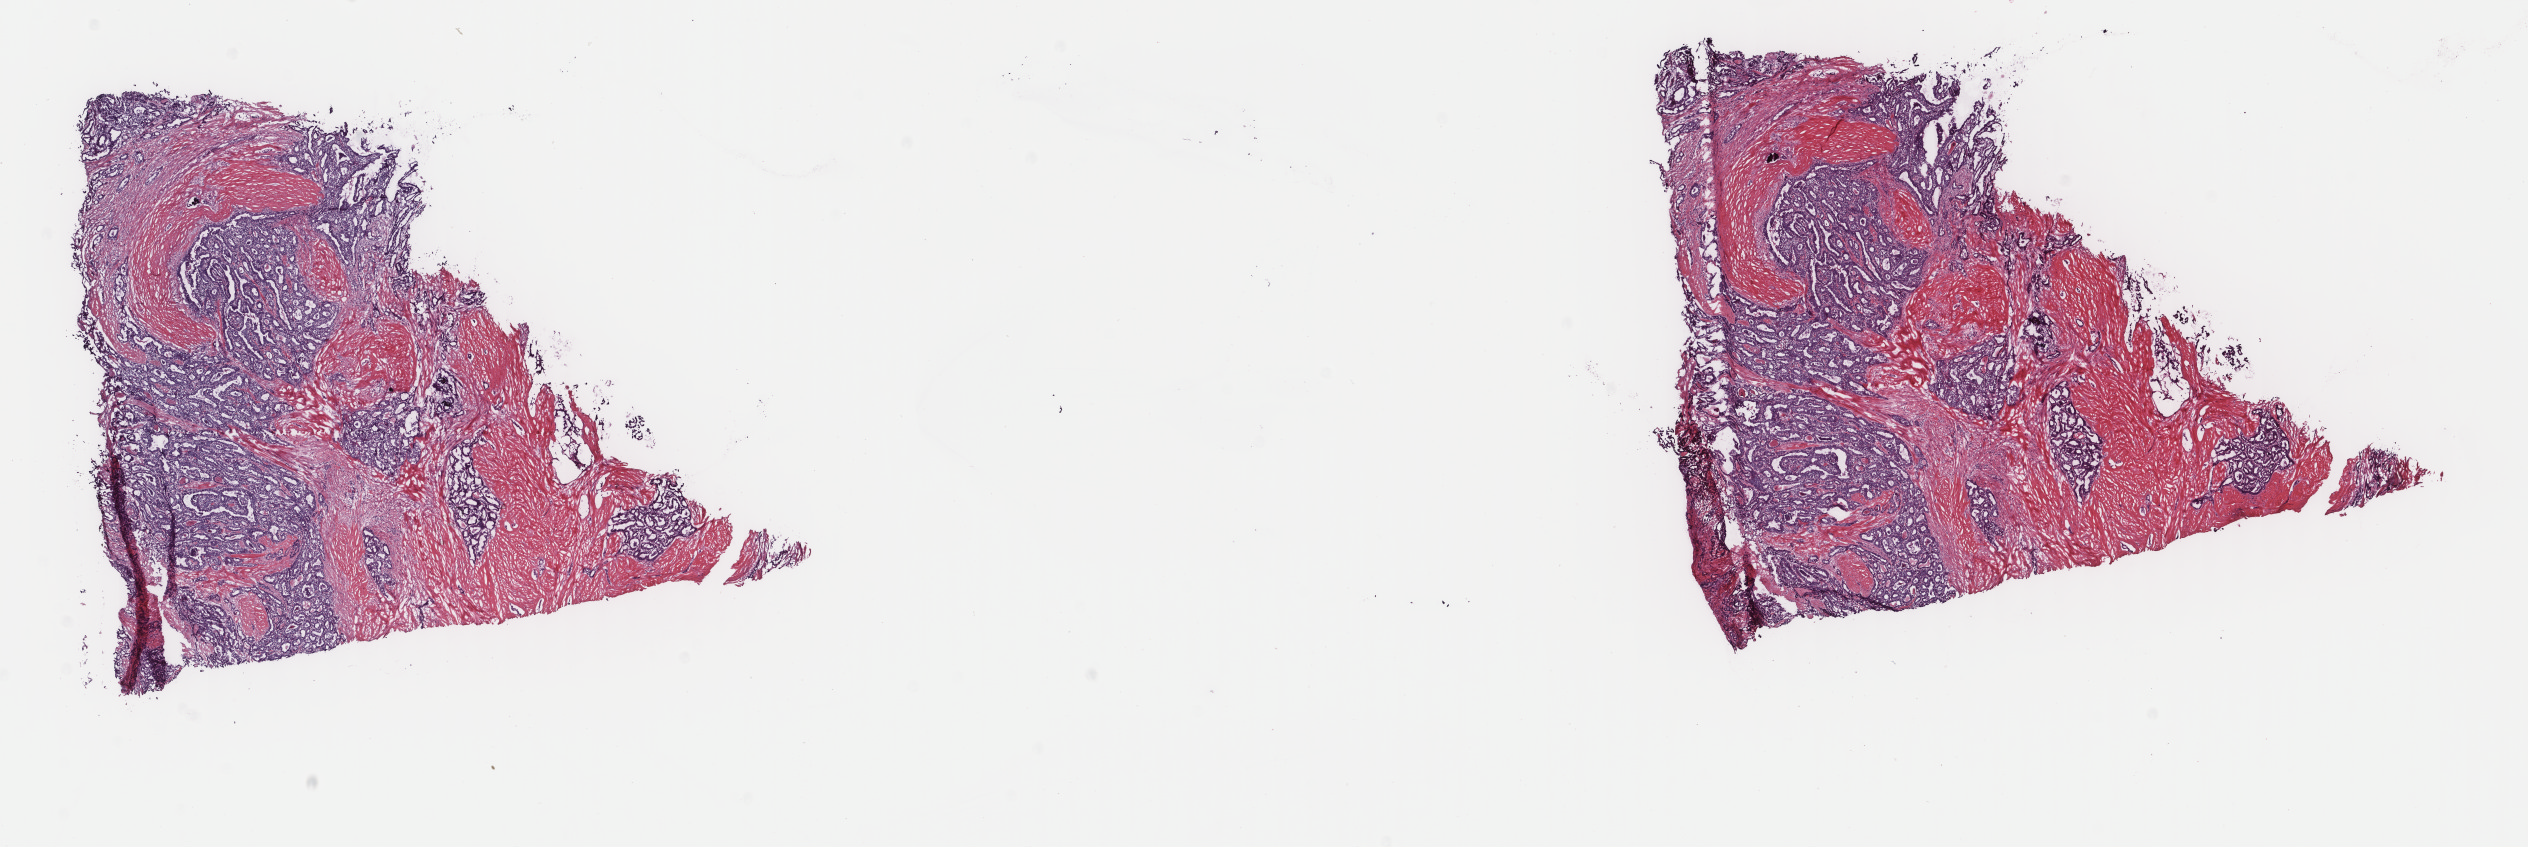
Whole-slide histology image, H&E, shown as a low-resolution overview of the whole scanned area (about 20.1 x 6.7 mm). Frozen section from the top of the tissue portion. Thyroid, primary tumour sample. Male patient; age at initial diagnosis 38 years. Slide review estimates, as recorded: tumour cells 75%, tumour nuclei 95%, normal cells 0%, stromal cells 25%, necrosis 0%. Infiltration values recorded for this section: lymphocyte infiltration 1%, monocyte infiltration 0%, neutrophil infiltration 0%.
- AJCC pathologic stage: I
- laterality: right
- diagnosis: Papillary carcinoma, columnar cell (thyroid gland)